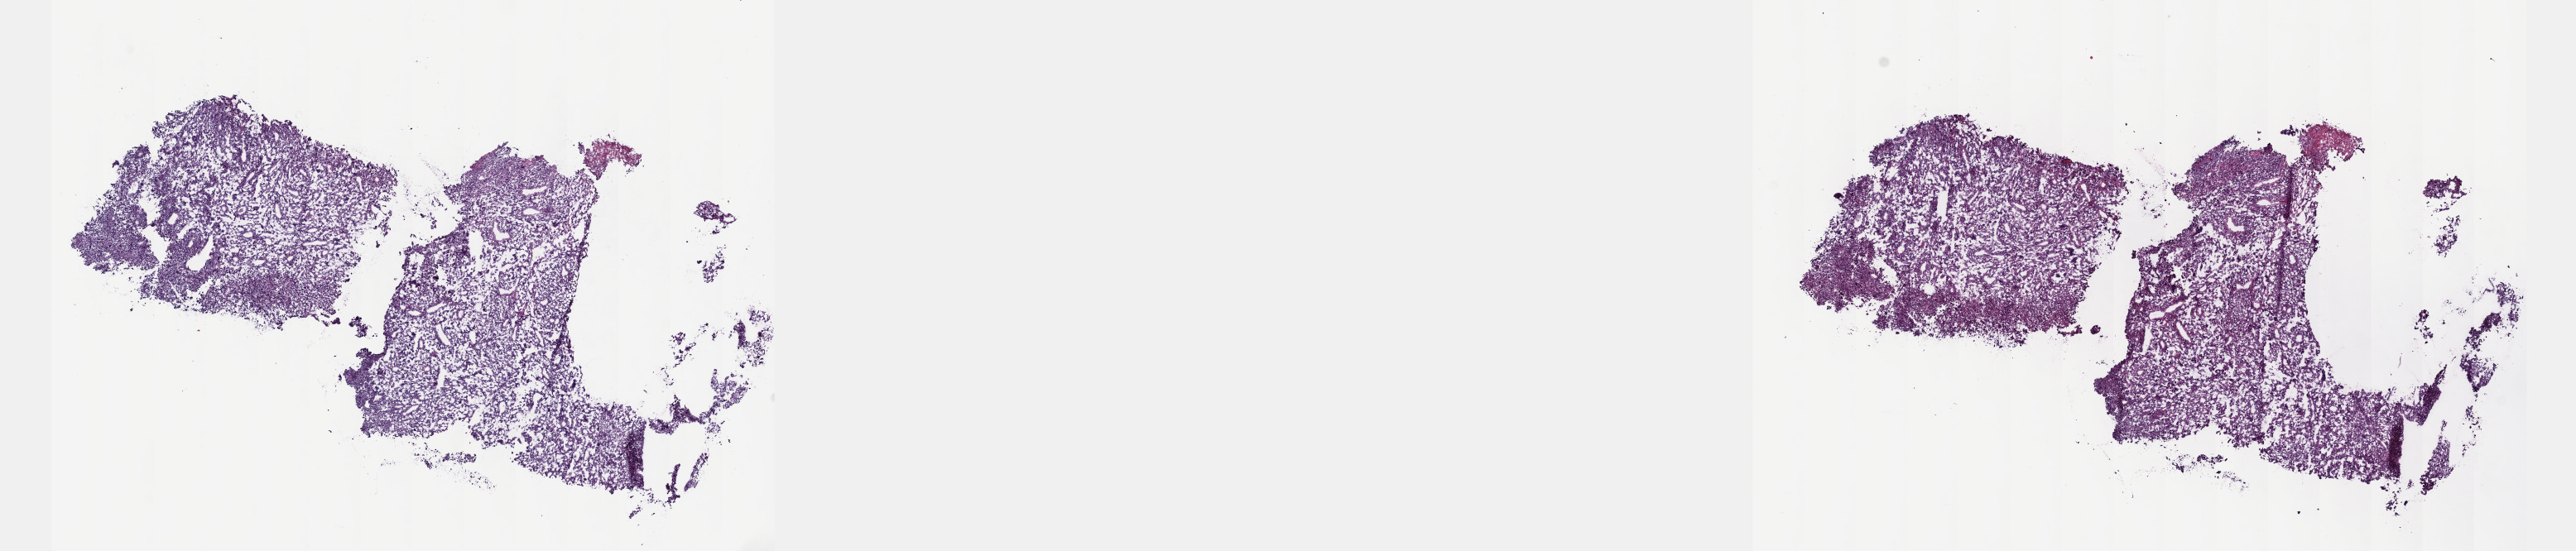
Whole-slide histology image, H&E-stained — whole scanned area (about 25.1 x 5.4 mm, acquisition: 40x scan) shown as a low-resolution overview; frozen section from the top of the tissue portion; metastatic tumour sample, sampled site not recorded. Male patient; age at initial diagnosis 63 years. Composition of this section per pathologist review: tumour cells 100%, tumour nuclei 80%, normal cells 0%, stromal cells 0%, necrosis 0%. Infiltration values recorded for this section: lymphocyte infiltration 2%, monocyte infiltration 0%, neutrophil infiltration 0%.
* this section: metastatic tumour tissue
* patient diagnosis: Malignant melanoma, NOS